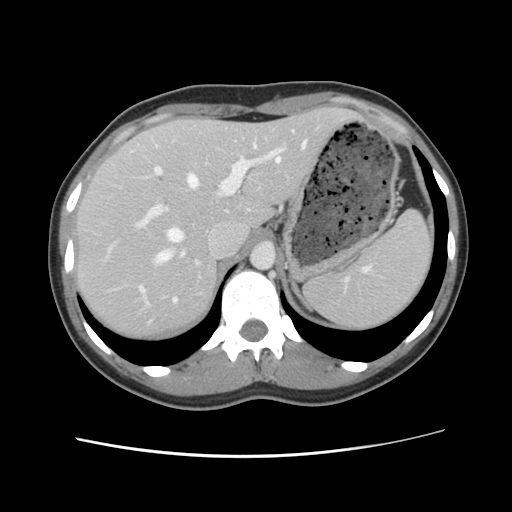
Contrast-enhanced abdominal CT, one axial slice; slice 82 of 134 in the series (ordered by position); 120 kVp; intravenous contrast given; soft-tissue window (W 400 / L 40 HU); 512 × 512 image matrix. Female patient, age 33 years. From the clinical record (not read from this slice): diagnosis: colorectal cancer liver metastases, imaged before liver resection; multiple liver metastases: yes; largest metastasis: 4.5 cm.
Outlined on this slice (expert manual segmentation):
- hepatic veins: bounding box [x1, y1, x2, y2] px = [140, 142, 306, 303]
- liver: [76, 109, 354, 341]
- planned liver remnant (the part of the liver to remain after resection): [76, 108, 354, 341]
- portal vein (with intrahepatic branches): [136, 138, 287, 227]